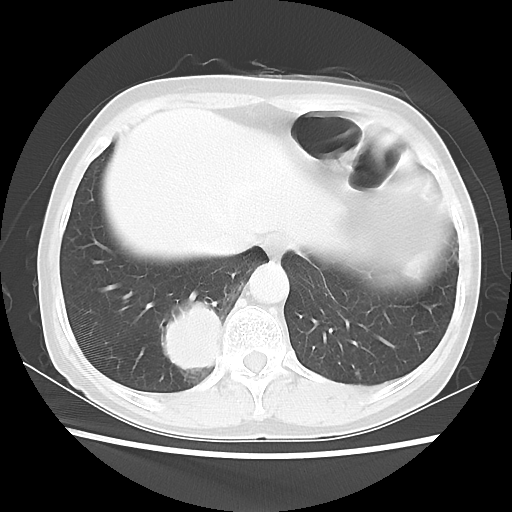
Chest CT, one axial slice; position 11 of 56 along the scan axis; reconstruction kernel LUNG; 120 kVp; lung window (W 1500 / L -600 HU); 5 mm slice thickness; 512 × 512 image matrix. Female patient, age 66 years. From the clinical record (not read from this slice): clinical TNM (as recorded): T2 N3 M0.
Annotated regions visible in this slice (bounding box drawn by a radiologist):
- lung tumour (recorded histology: small cell carcinoma): bounding box [x1, y1, x2, y2] px = [150, 295, 234, 380]